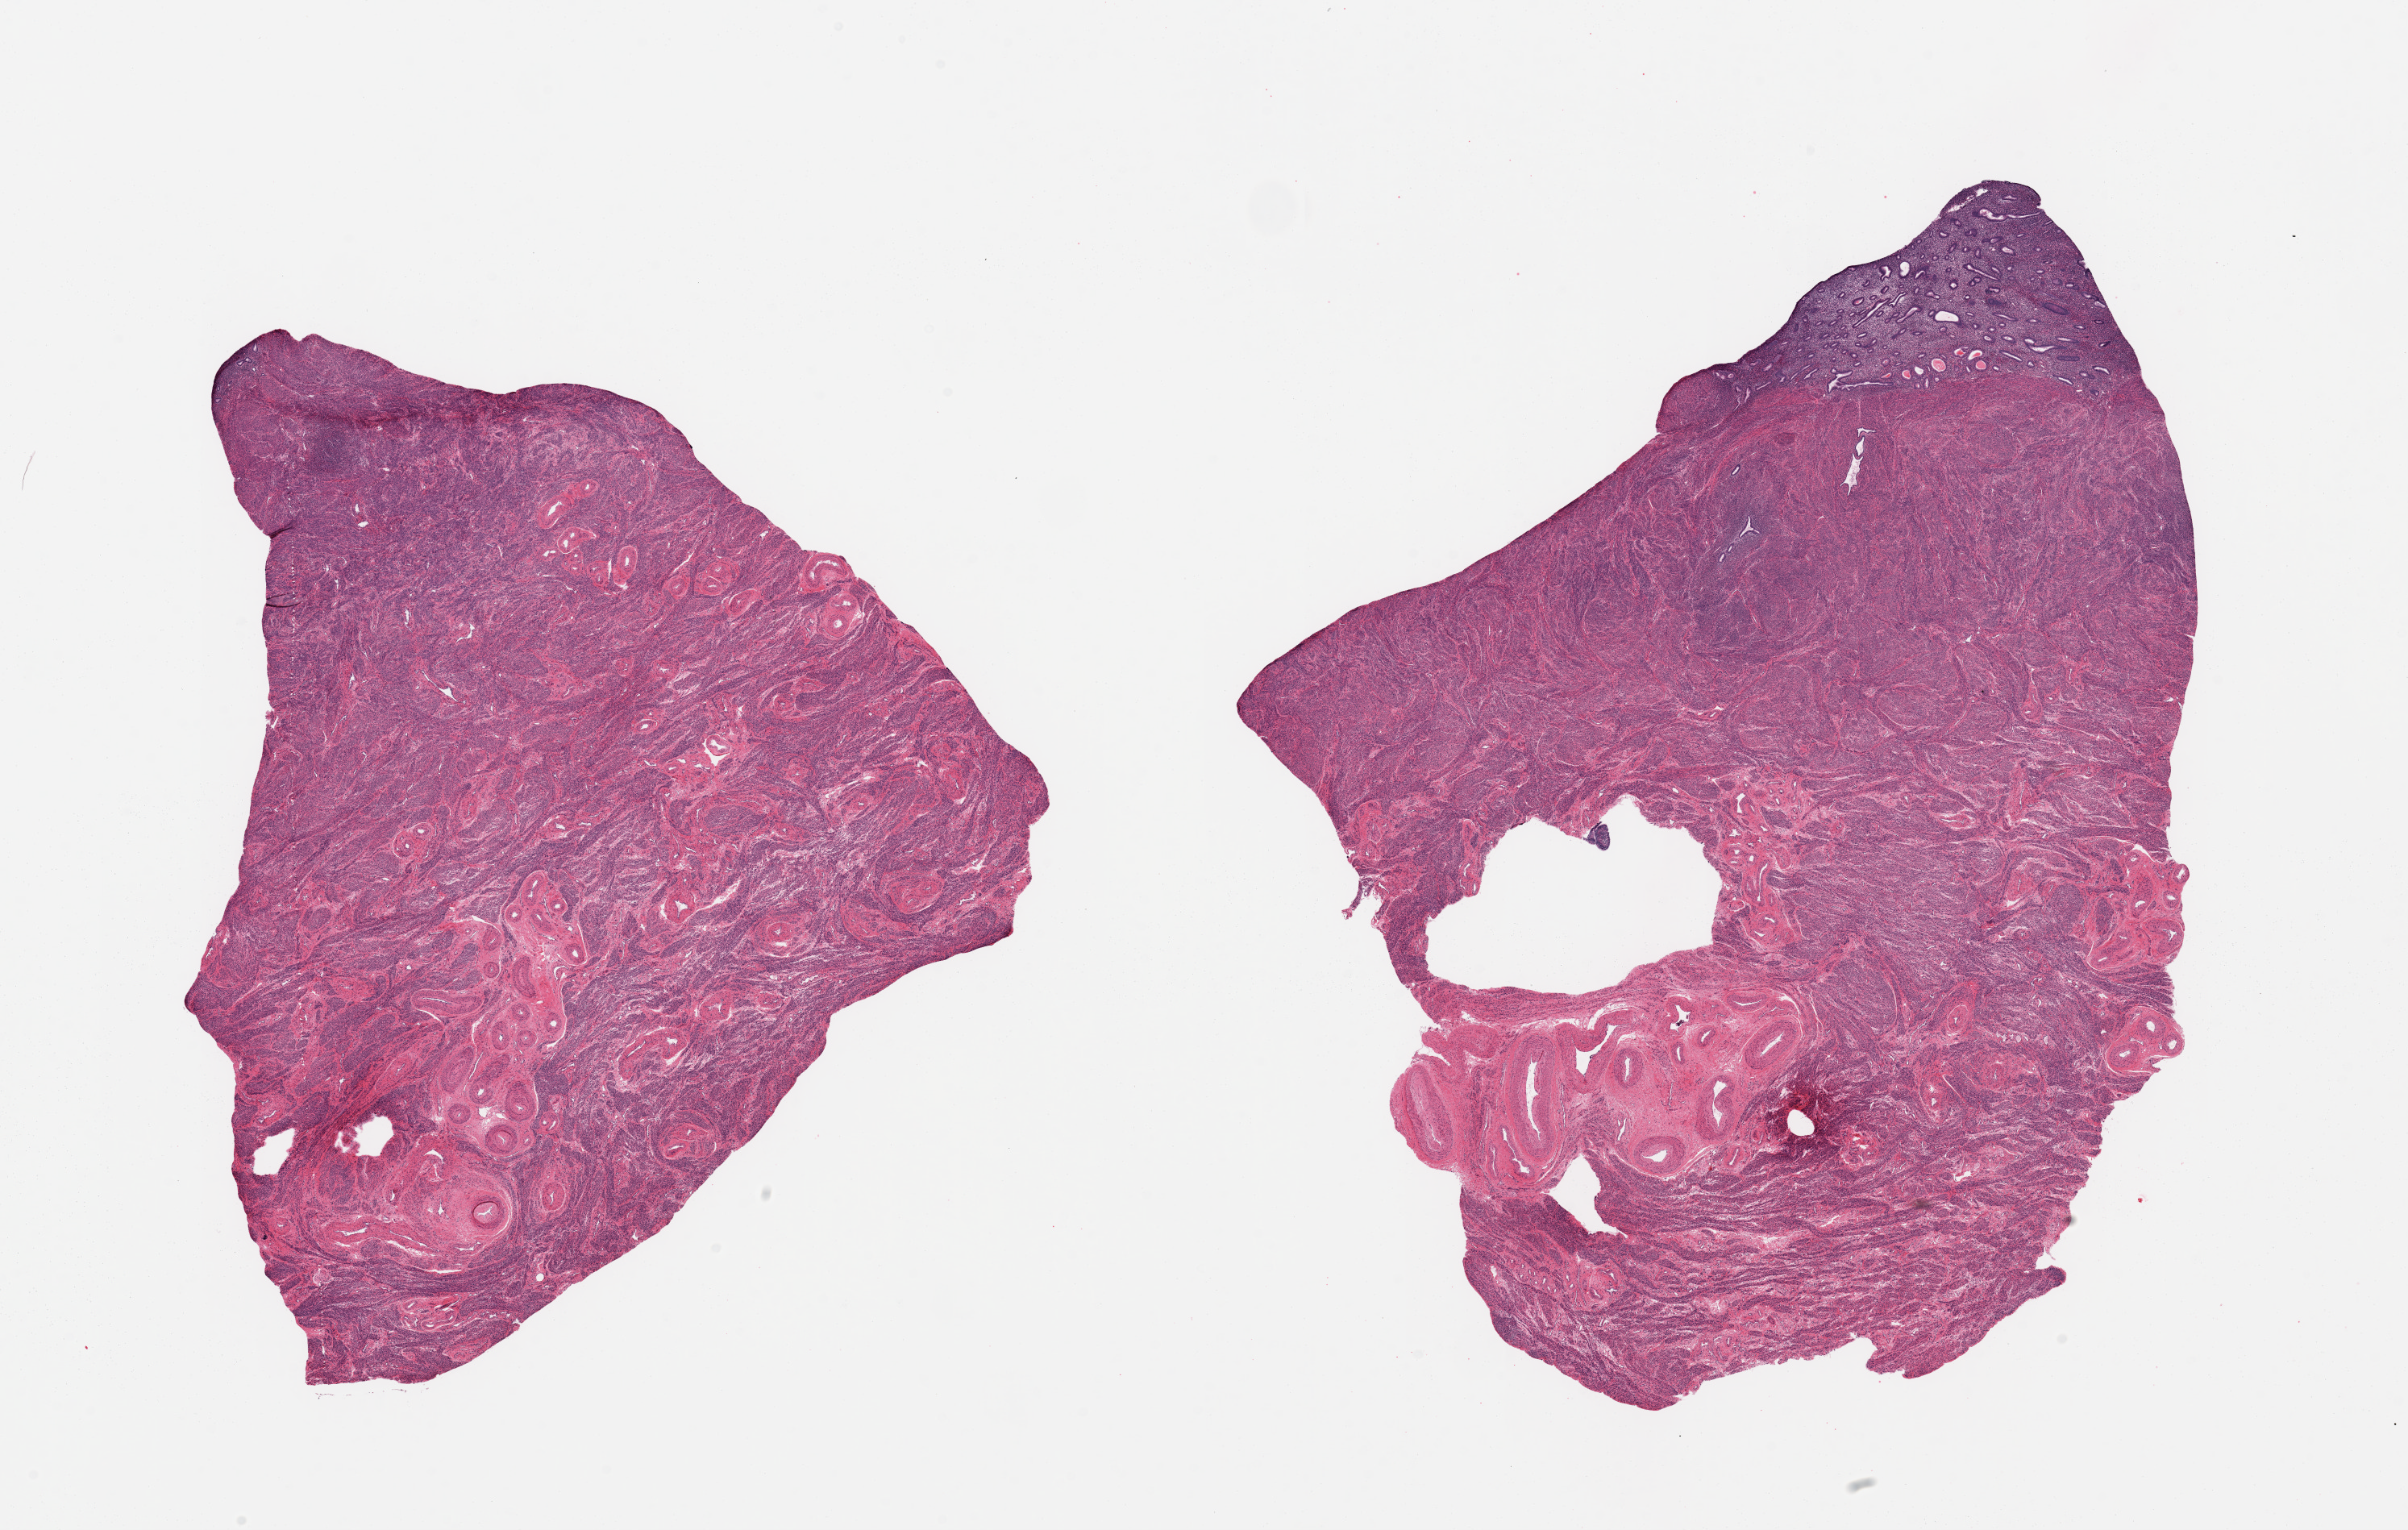
Whole-slide image, H&E stain — shown as a low-resolution overview of the whole scanned area (about 23.6 x 15.0 mm), PAXgene-fixed, paraffin-embedded tissue, target tissue: uterus, tissue donor sample.
Review note (as recorded): 2 pieces; small amount of proliferative endometrium in each piece.